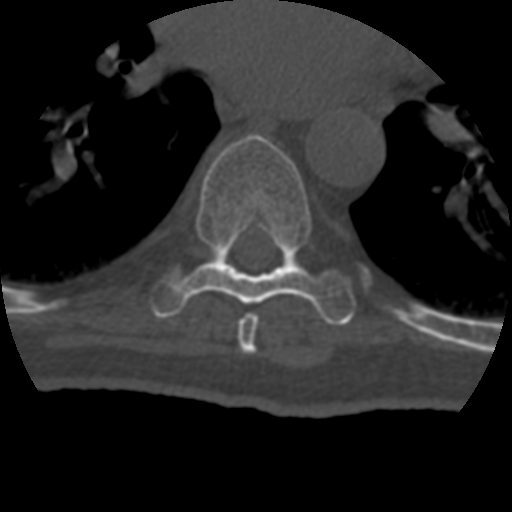
CT including the spine, one axial slice; slice 261 of 399 in the series (ordered by position); bone window (W 1800 / L 400 HU); 1.25 mm slice thickness; 512 × 512 image matrix. Patient age 69 years. Case-level facts recorded for this patient, not image findings: primary cancer: prostate.
Annotated regions visible in this slice (semi-automatically segmented with operator editing):
- T7 vertebra: box from (x=238, y=313) to (x=259, y=354) px
- T8 vertebra: (x=150, y=134)–(x=356, y=325)